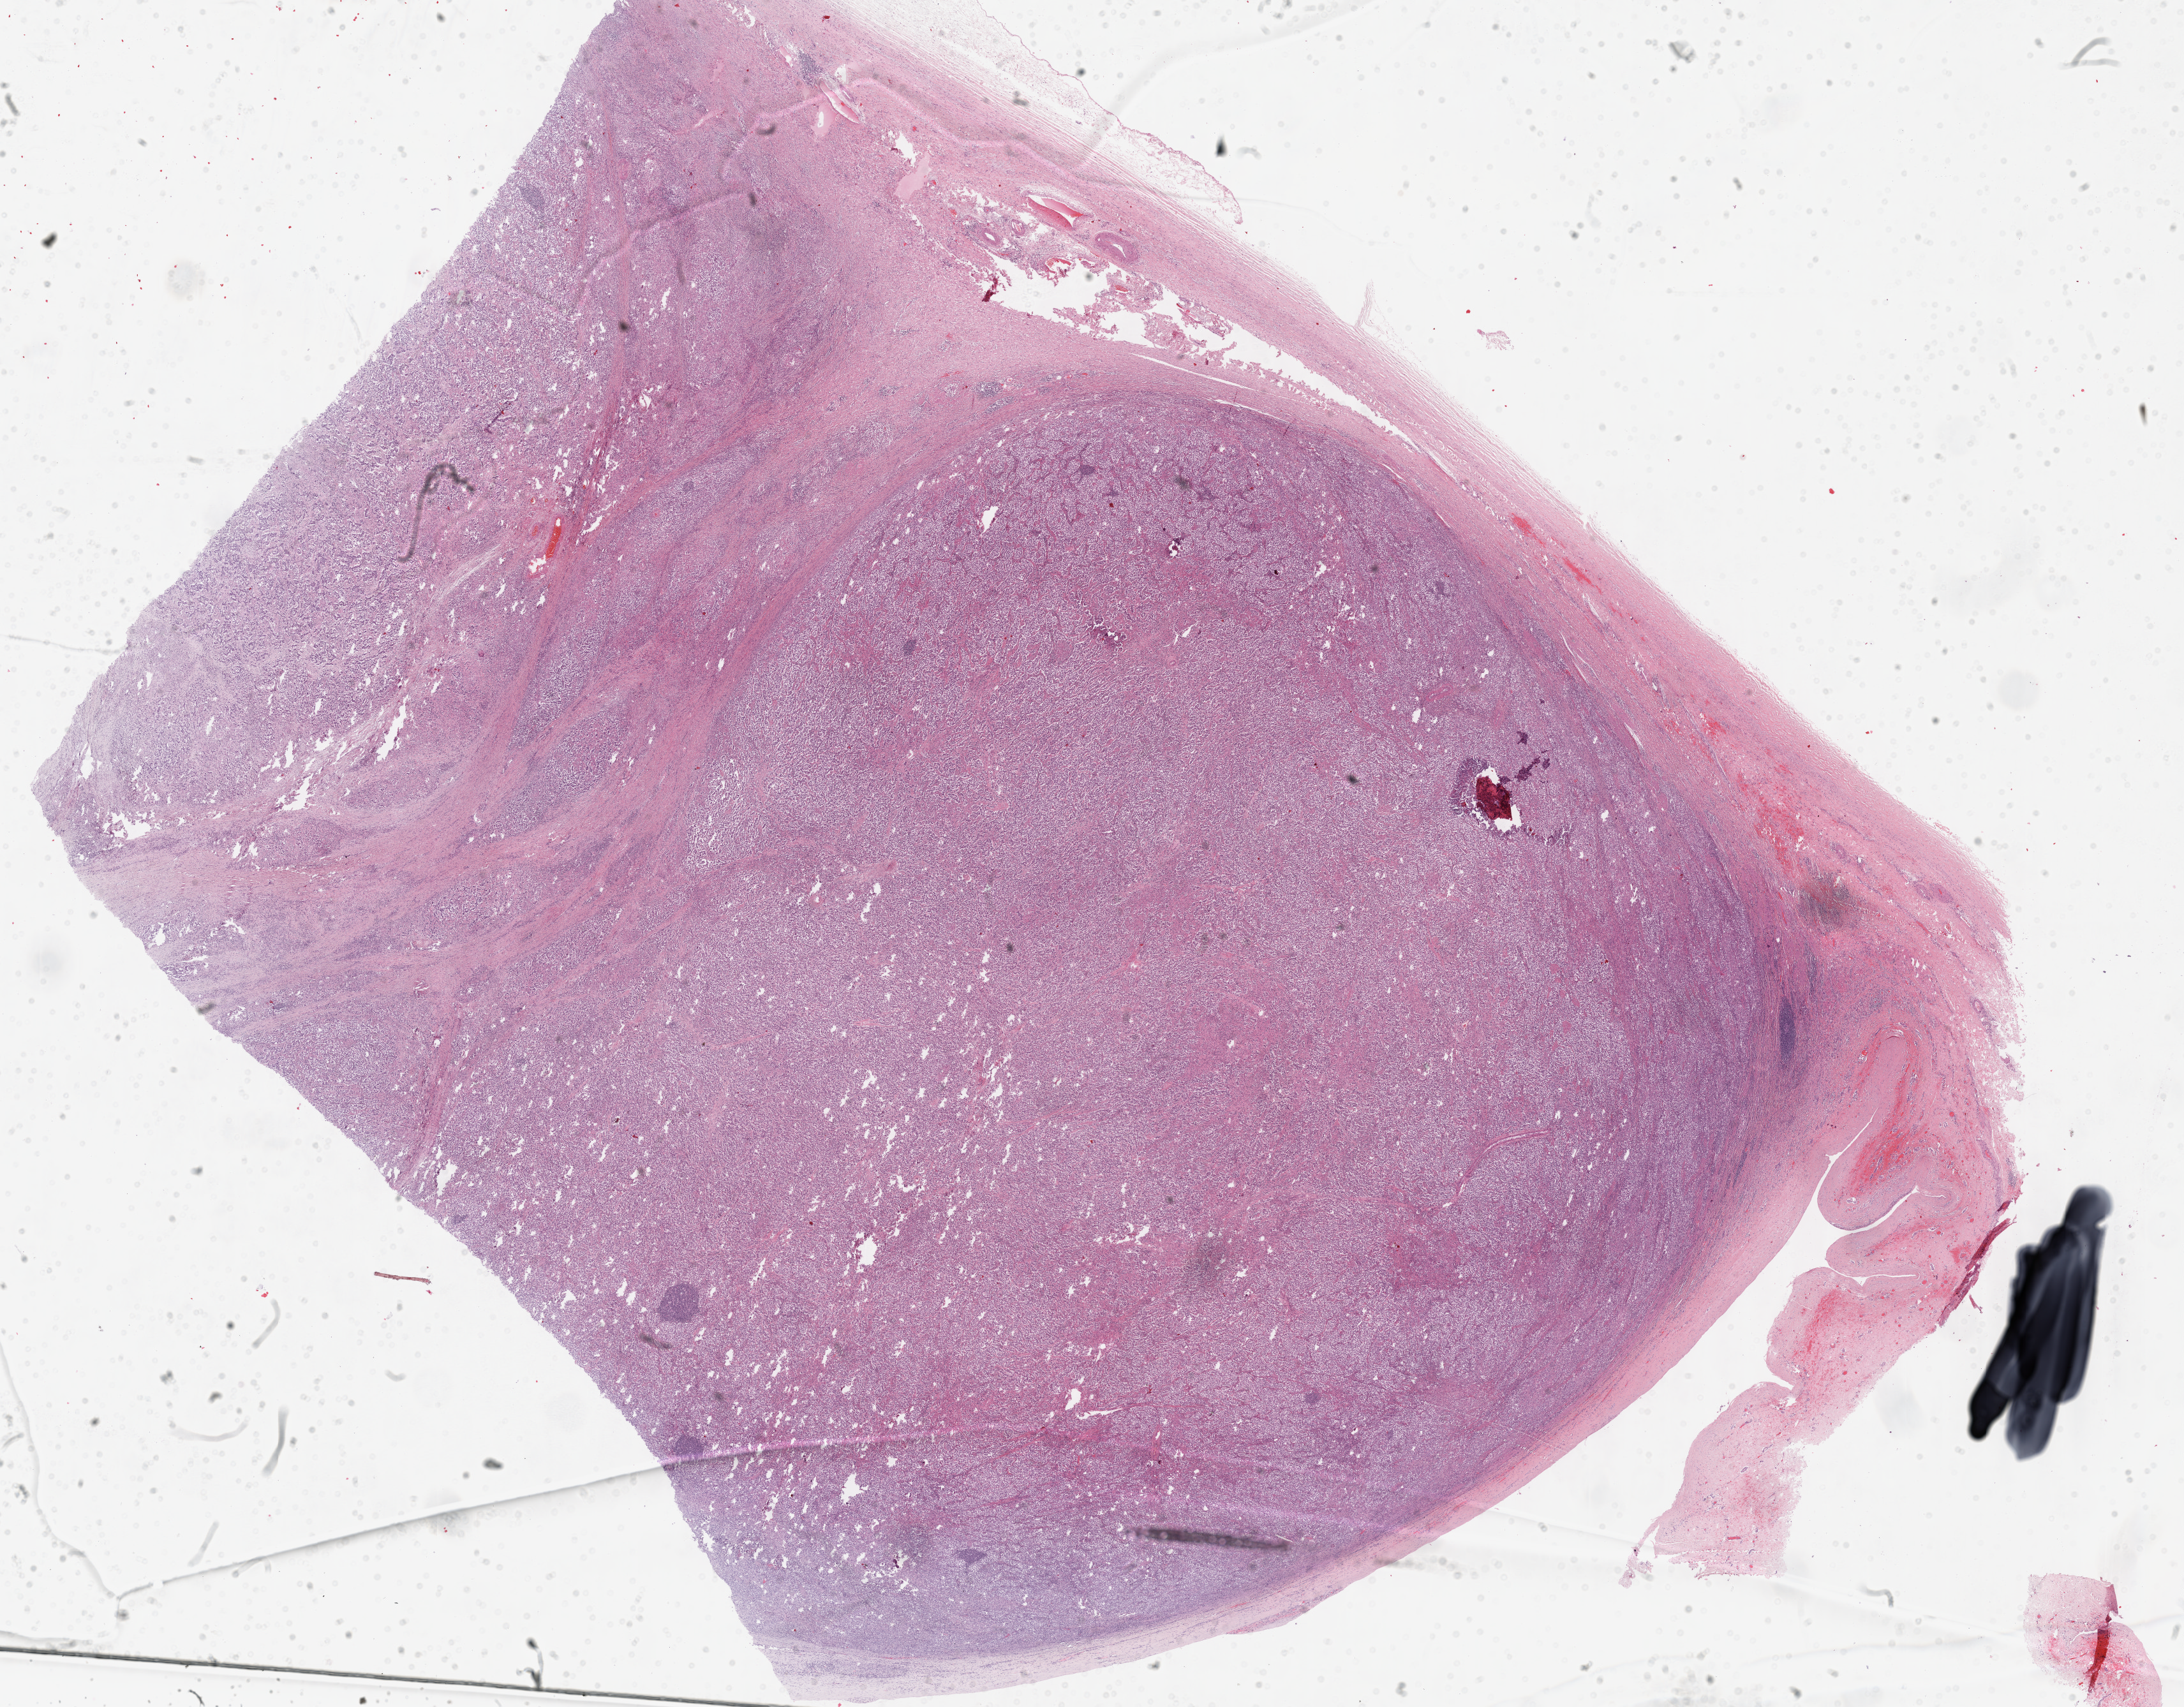
Digitized H&E-stained tissue section (whole slide) — a low-resolution overview of the entire scanned area, about 27.7 x 21.6 mm (from a 40x scan). Formalin-fixed paraffin-embedded (FFPE) diagnostic section. Primary tumour sample from the testis. Patient: male, age at initial diagnosis 36 years.
- diagnosis: Seminoma, NOS
- AJCC pathologic stage: IIC